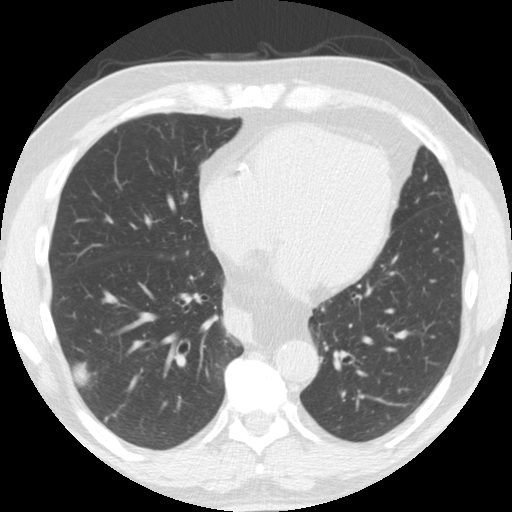
Low-dose screening chest CT, axial slice. Second screening round (one year after baseline). Lung window (W 1500 / L -600 HU). 2.5 mm slice thickness. 120 kVp. Slice 107 of 174 in the series. Male participant, aged 61 years at enrolment. Former smoker at enrolment.
• Expert-annotated lung lesion, bounding box <42,320,110,398> (left, top, right, bottom; pixels).
• The exam's reader record, not a measurement of the box and not confirmed to be the same lesion: non-calcified nodule or mass ≥4 mm, right lower lobe, 33 × 19 mm, smooth margins, soft tissue attenuation, pre-existing on the prior screen: yes; interval growth: yes.
• Official screen result: positive, change unspecified: nodule(s) >= 4 mm or enlarging nodule(s), mass(es), or other non-specific abnormalities suspicious for lung cancer.
• Participant outcome: lung cancer diagnosed 30 days after this screen — adenosquamous carcinoma, right lower lobe, poorly differentiated (G3), stage IV (AJCC 6th edition), 45 mm at pathology.